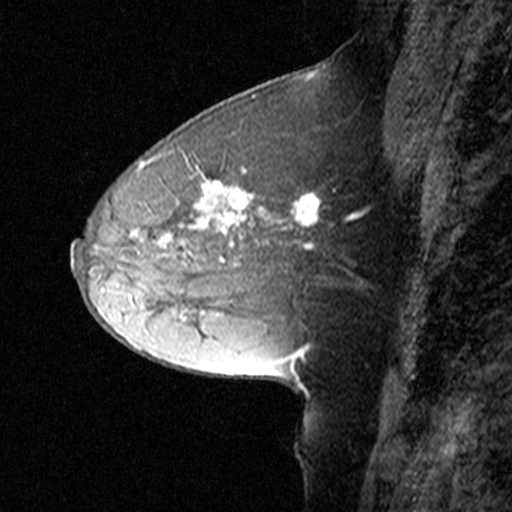
Breast MRI (dynamic contrast-enhanced), one sagittal slice; slice 20 of 44 in the series (ordered by position); dynamic contrast-enhanced study with each time point stored as its own series, time point 2 of 3 at this slice position (early post-contrast, ordered by acquisition time); 1.5 T; TE 4.5 ms, TR 11 ms; 3 mm slice thickness; 512 × 512 image matrix, field of view 200 × 200 mm. Female patient, age 50 years. From the clinical record (not read from this slice): setting: breast cancer imaged before/during neoadjuvant chemotherapy; receptor status: HR-positive, HER2-negative.
Annotated regions visible in this slice (semi-automatic segmentation, software-assisted and operator-edited):
- analysis volume of interest (the breast-tissue region the enhancement analysis was run in; not a lesion): bounding box <126,162,329,291> (left, top, right, bottom; pixels)
- tumour enhancement mask (voxels above the 90 % enhancement threshold inside the analysis volume of interest): <131,162,326,263>